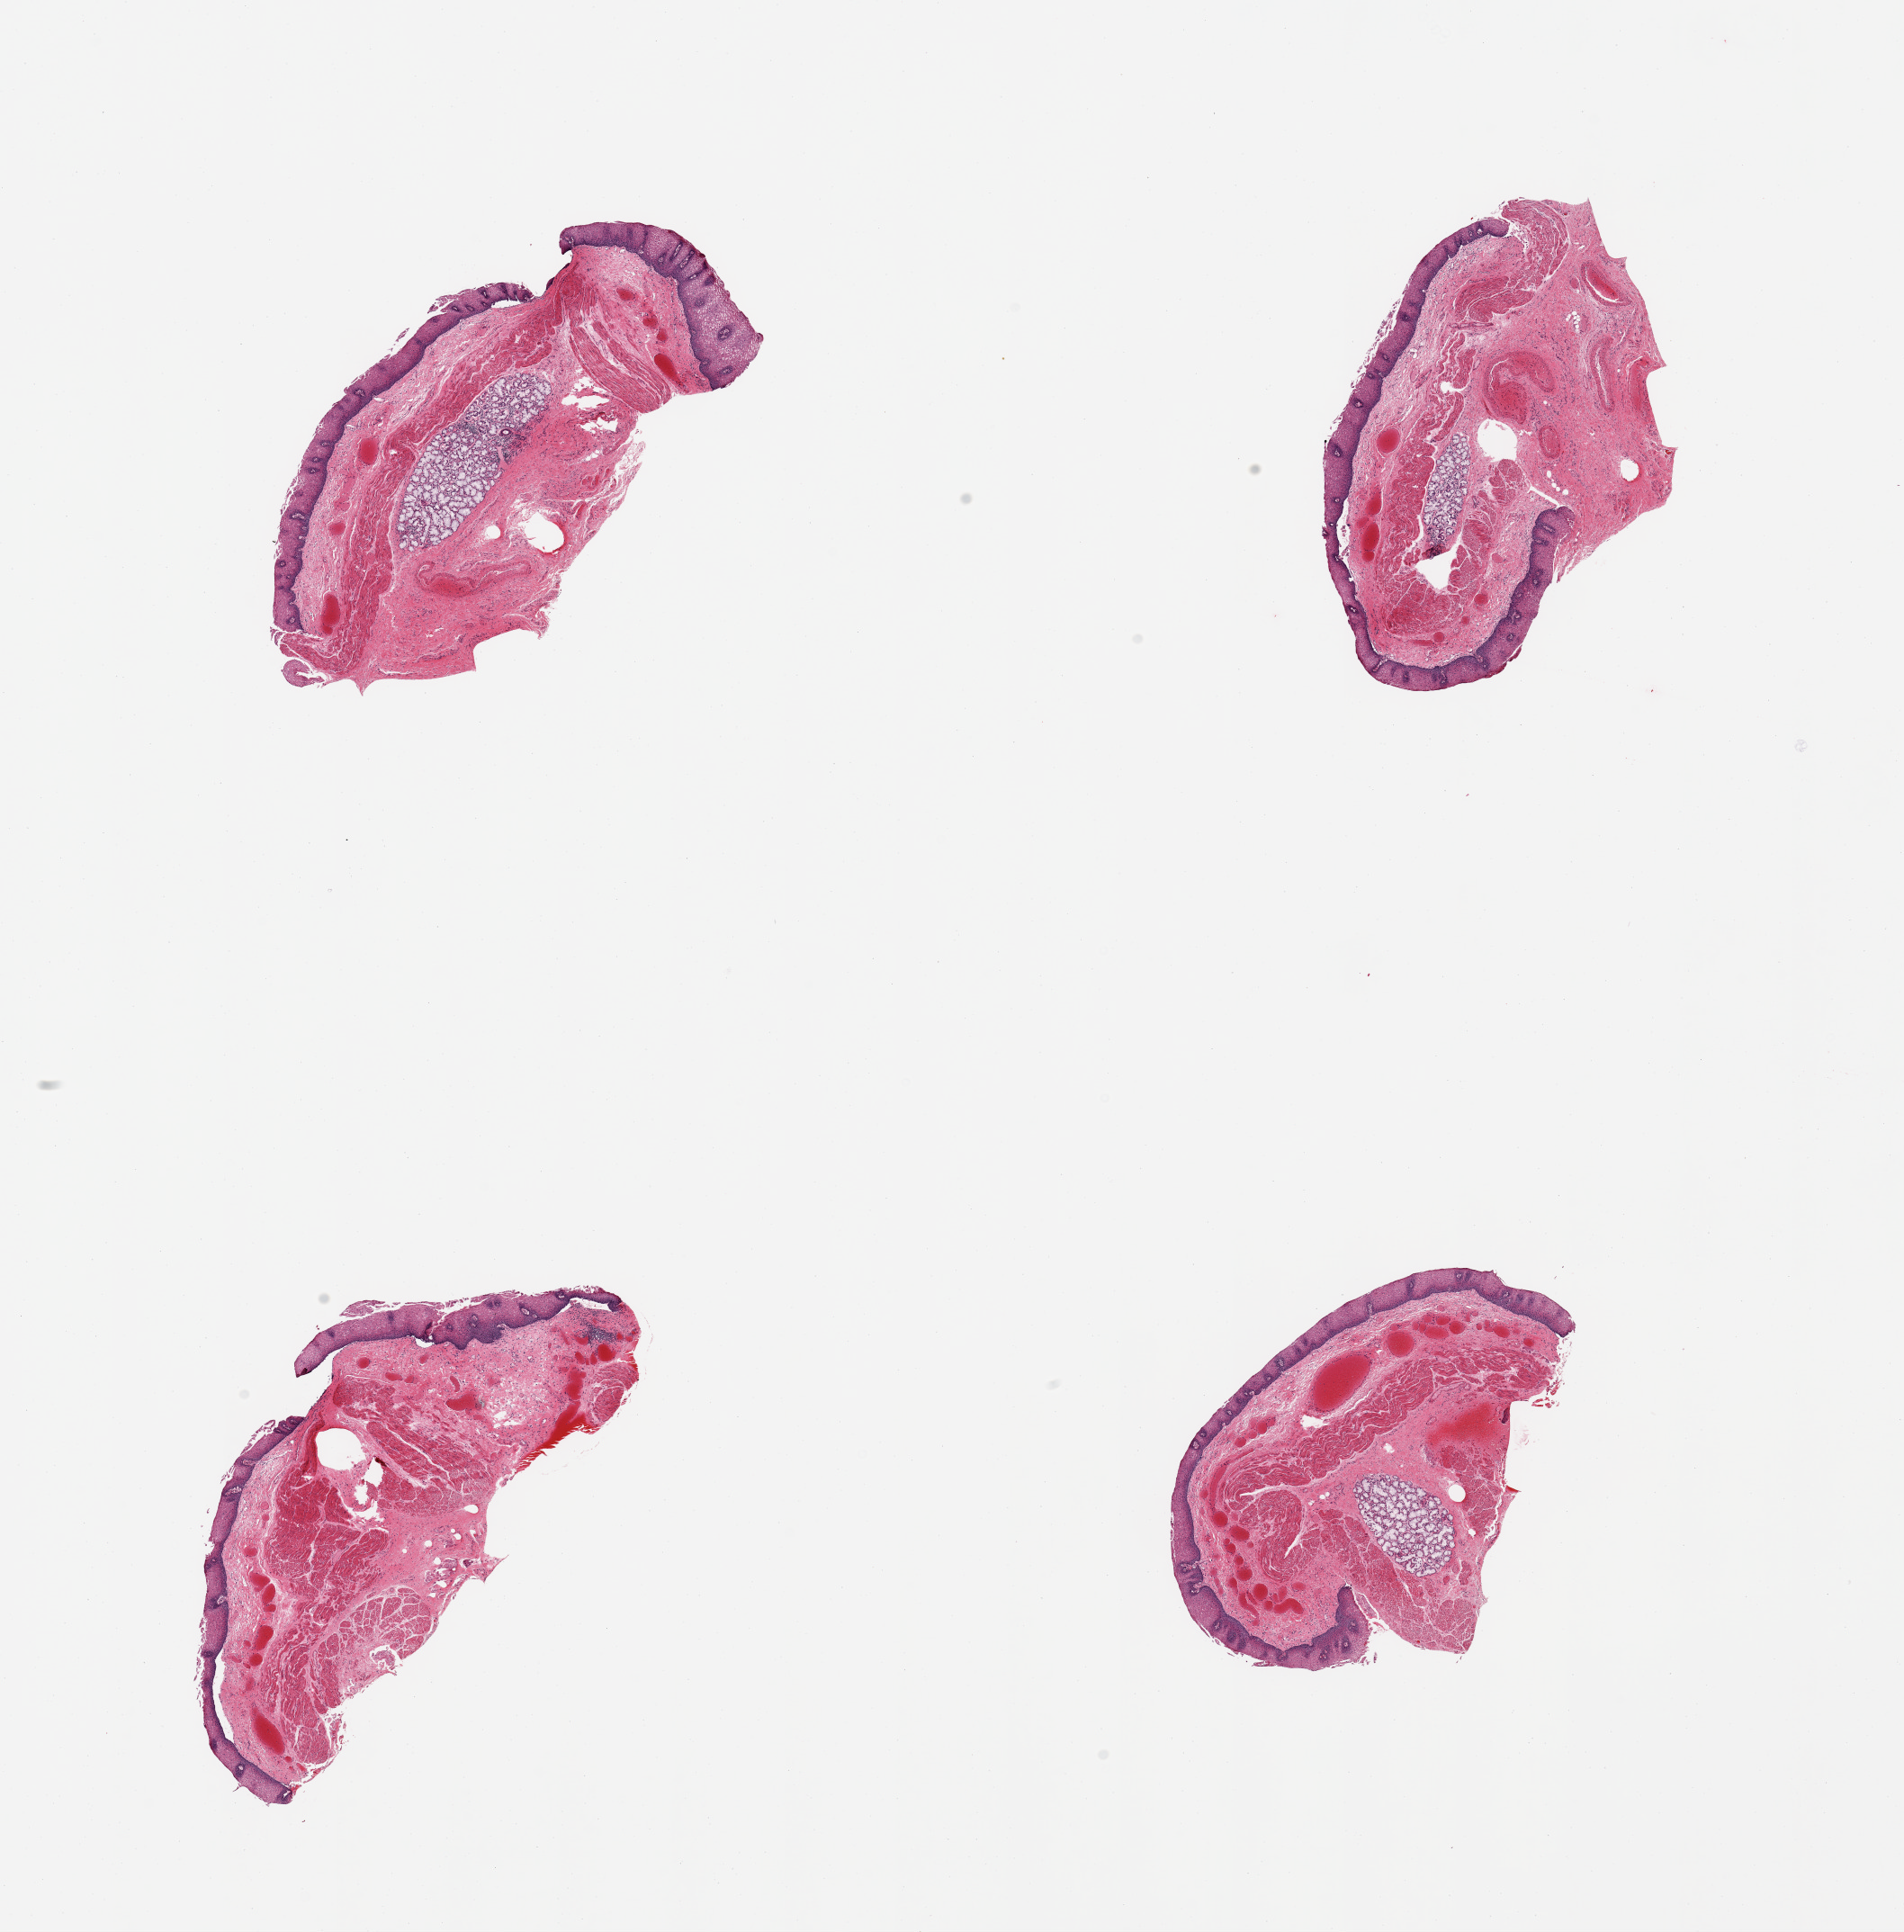
H&E whole-slide image — whole scanned area (about 16.7 x 17.0 mm, from a 20x scan) shown as a low-resolution overview. PAXgene-fixed paraffin-embedded (PFPE) section. Sampled site (target tissue): esophageal mucous membrane. Donor tissue sample.
Review note (as recorded): 4 pieces; large [up to 1.8x0.5mm] submucosal glands in 3 pieces, congestion and 161um thick squamous epithelium.